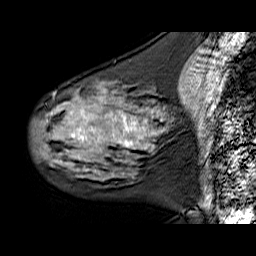
Breast MRI (dynamic contrast-enhanced), one sagittal slice. Slice 22 of 60 in the series (ordered by position). Dynamic contrast-enhanced series, time point 2 of 6 at this slice position (early post-contrast). 1.5 T. TE 6.3 ms, TR 32.9 ms. 4 mm slice thickness. 256 × 256 image matrix, field of view 200 × 200 mm. Female patient. Case-level facts recorded for this patient, not image findings: setting: breast cancer imaged before/during neoadjuvant chemotherapy; receptor status: HER2-positive.
Annotated regions visible in this slice (semi-automatic segmentation, software-assisted and operator-edited):
- analysis volume of interest (the breast-tissue region the enhancement analysis was run in; not a lesion): bounding box [x1, y1, x2, y2] px = [33, 81, 171, 180]
- tumour enhancement mask (voxels above the 100 % enhancement threshold inside the analysis volume of interest): [72, 116, 146, 147]